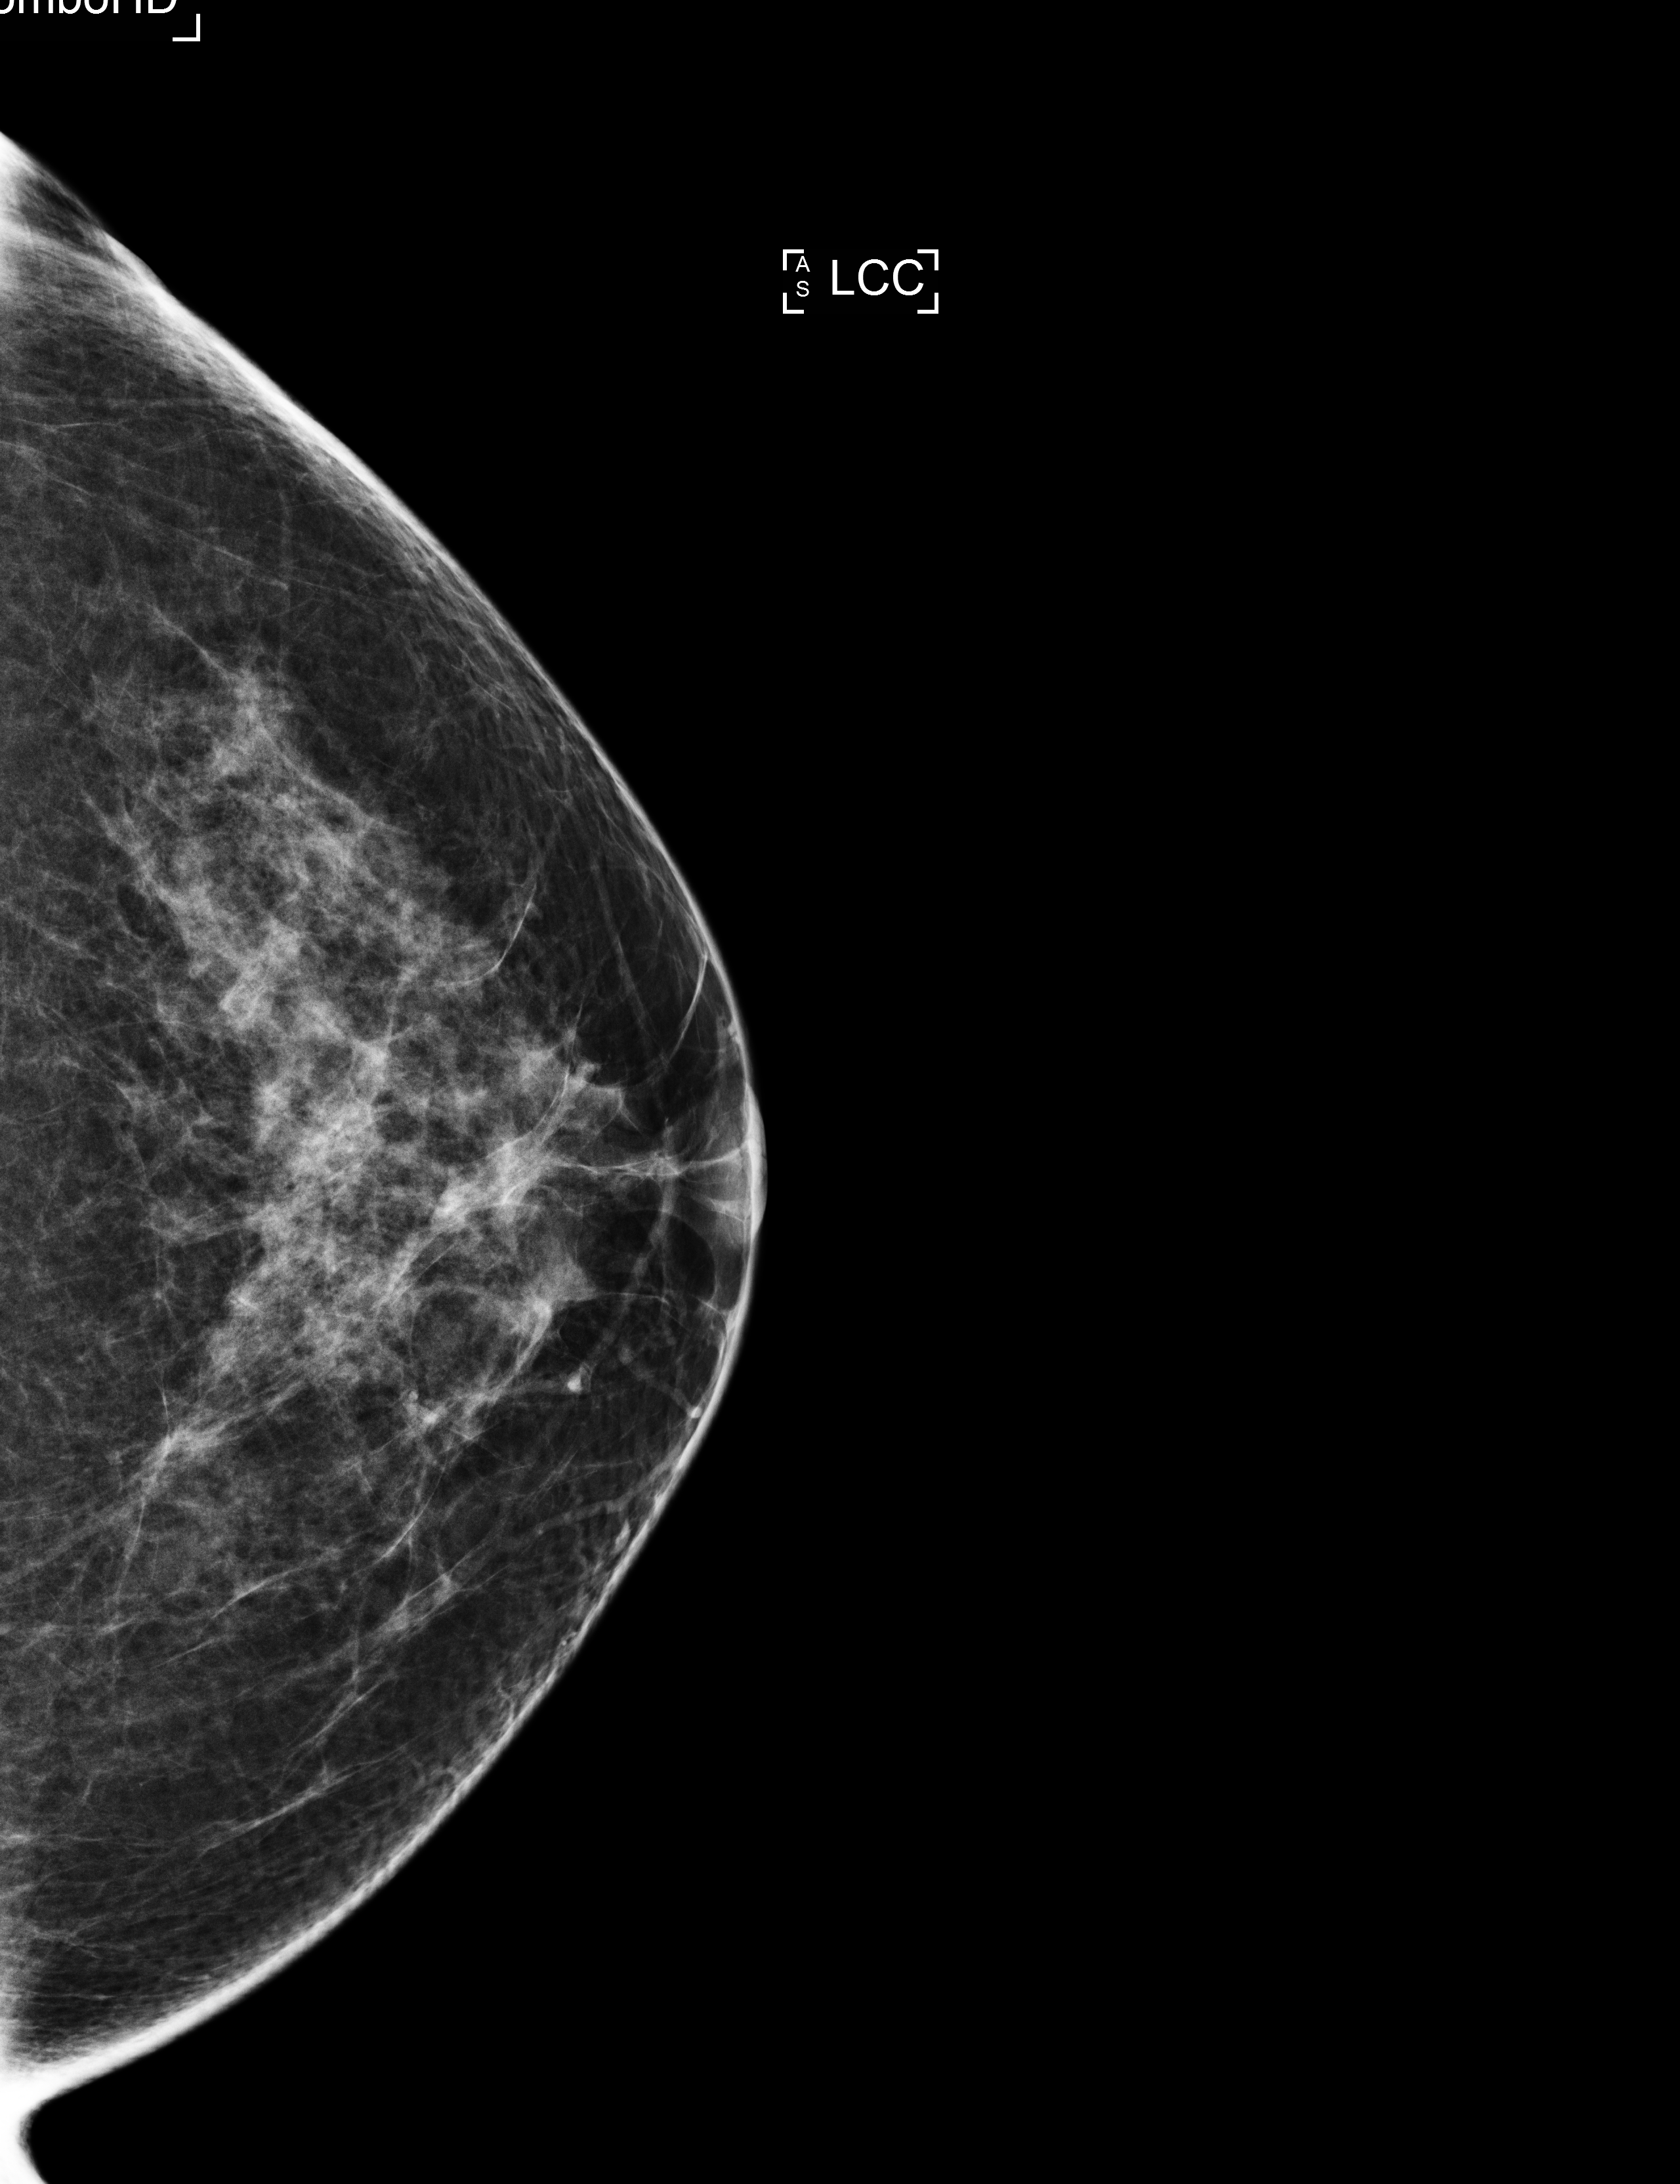
Full-field digital mammogram (FFDM); left breast; cranio-caudal projection; annual screening mammography examination; system: Selenia Dimensions. Female patient, age 44 years.
Final BI-RADS assessment for this screening round (tomosynthesis exam, both breasts): category 1.